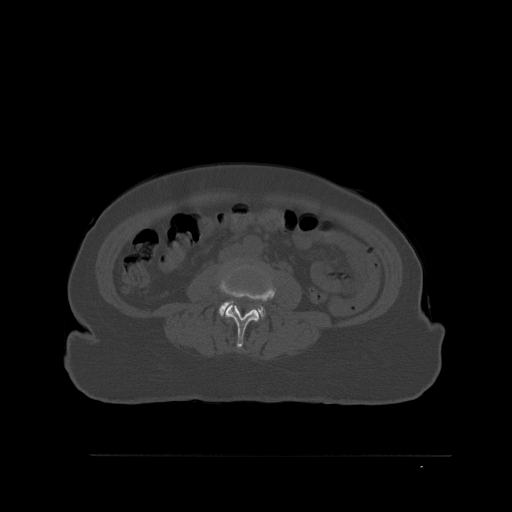
CT including the spine, one axial slice; slice 220 of 527 in the series (ordered by position); bone window (W 1800 / L 400 HU); 512 × 512 image matrix. Female patient, age 73 years. From the clinical record (not read from this slice): primary cancer: breast; vertebrae with lytic lesions (as recorded): L2.
Annotated regions visible in this slice (semi-automatic segmentation, software-assisted and operator-edited):
- L3 vertebra: bounding box <219,262,277,348> (left, top, right, bottom; pixels)
- L4 vertebra: <219,301,266,320>